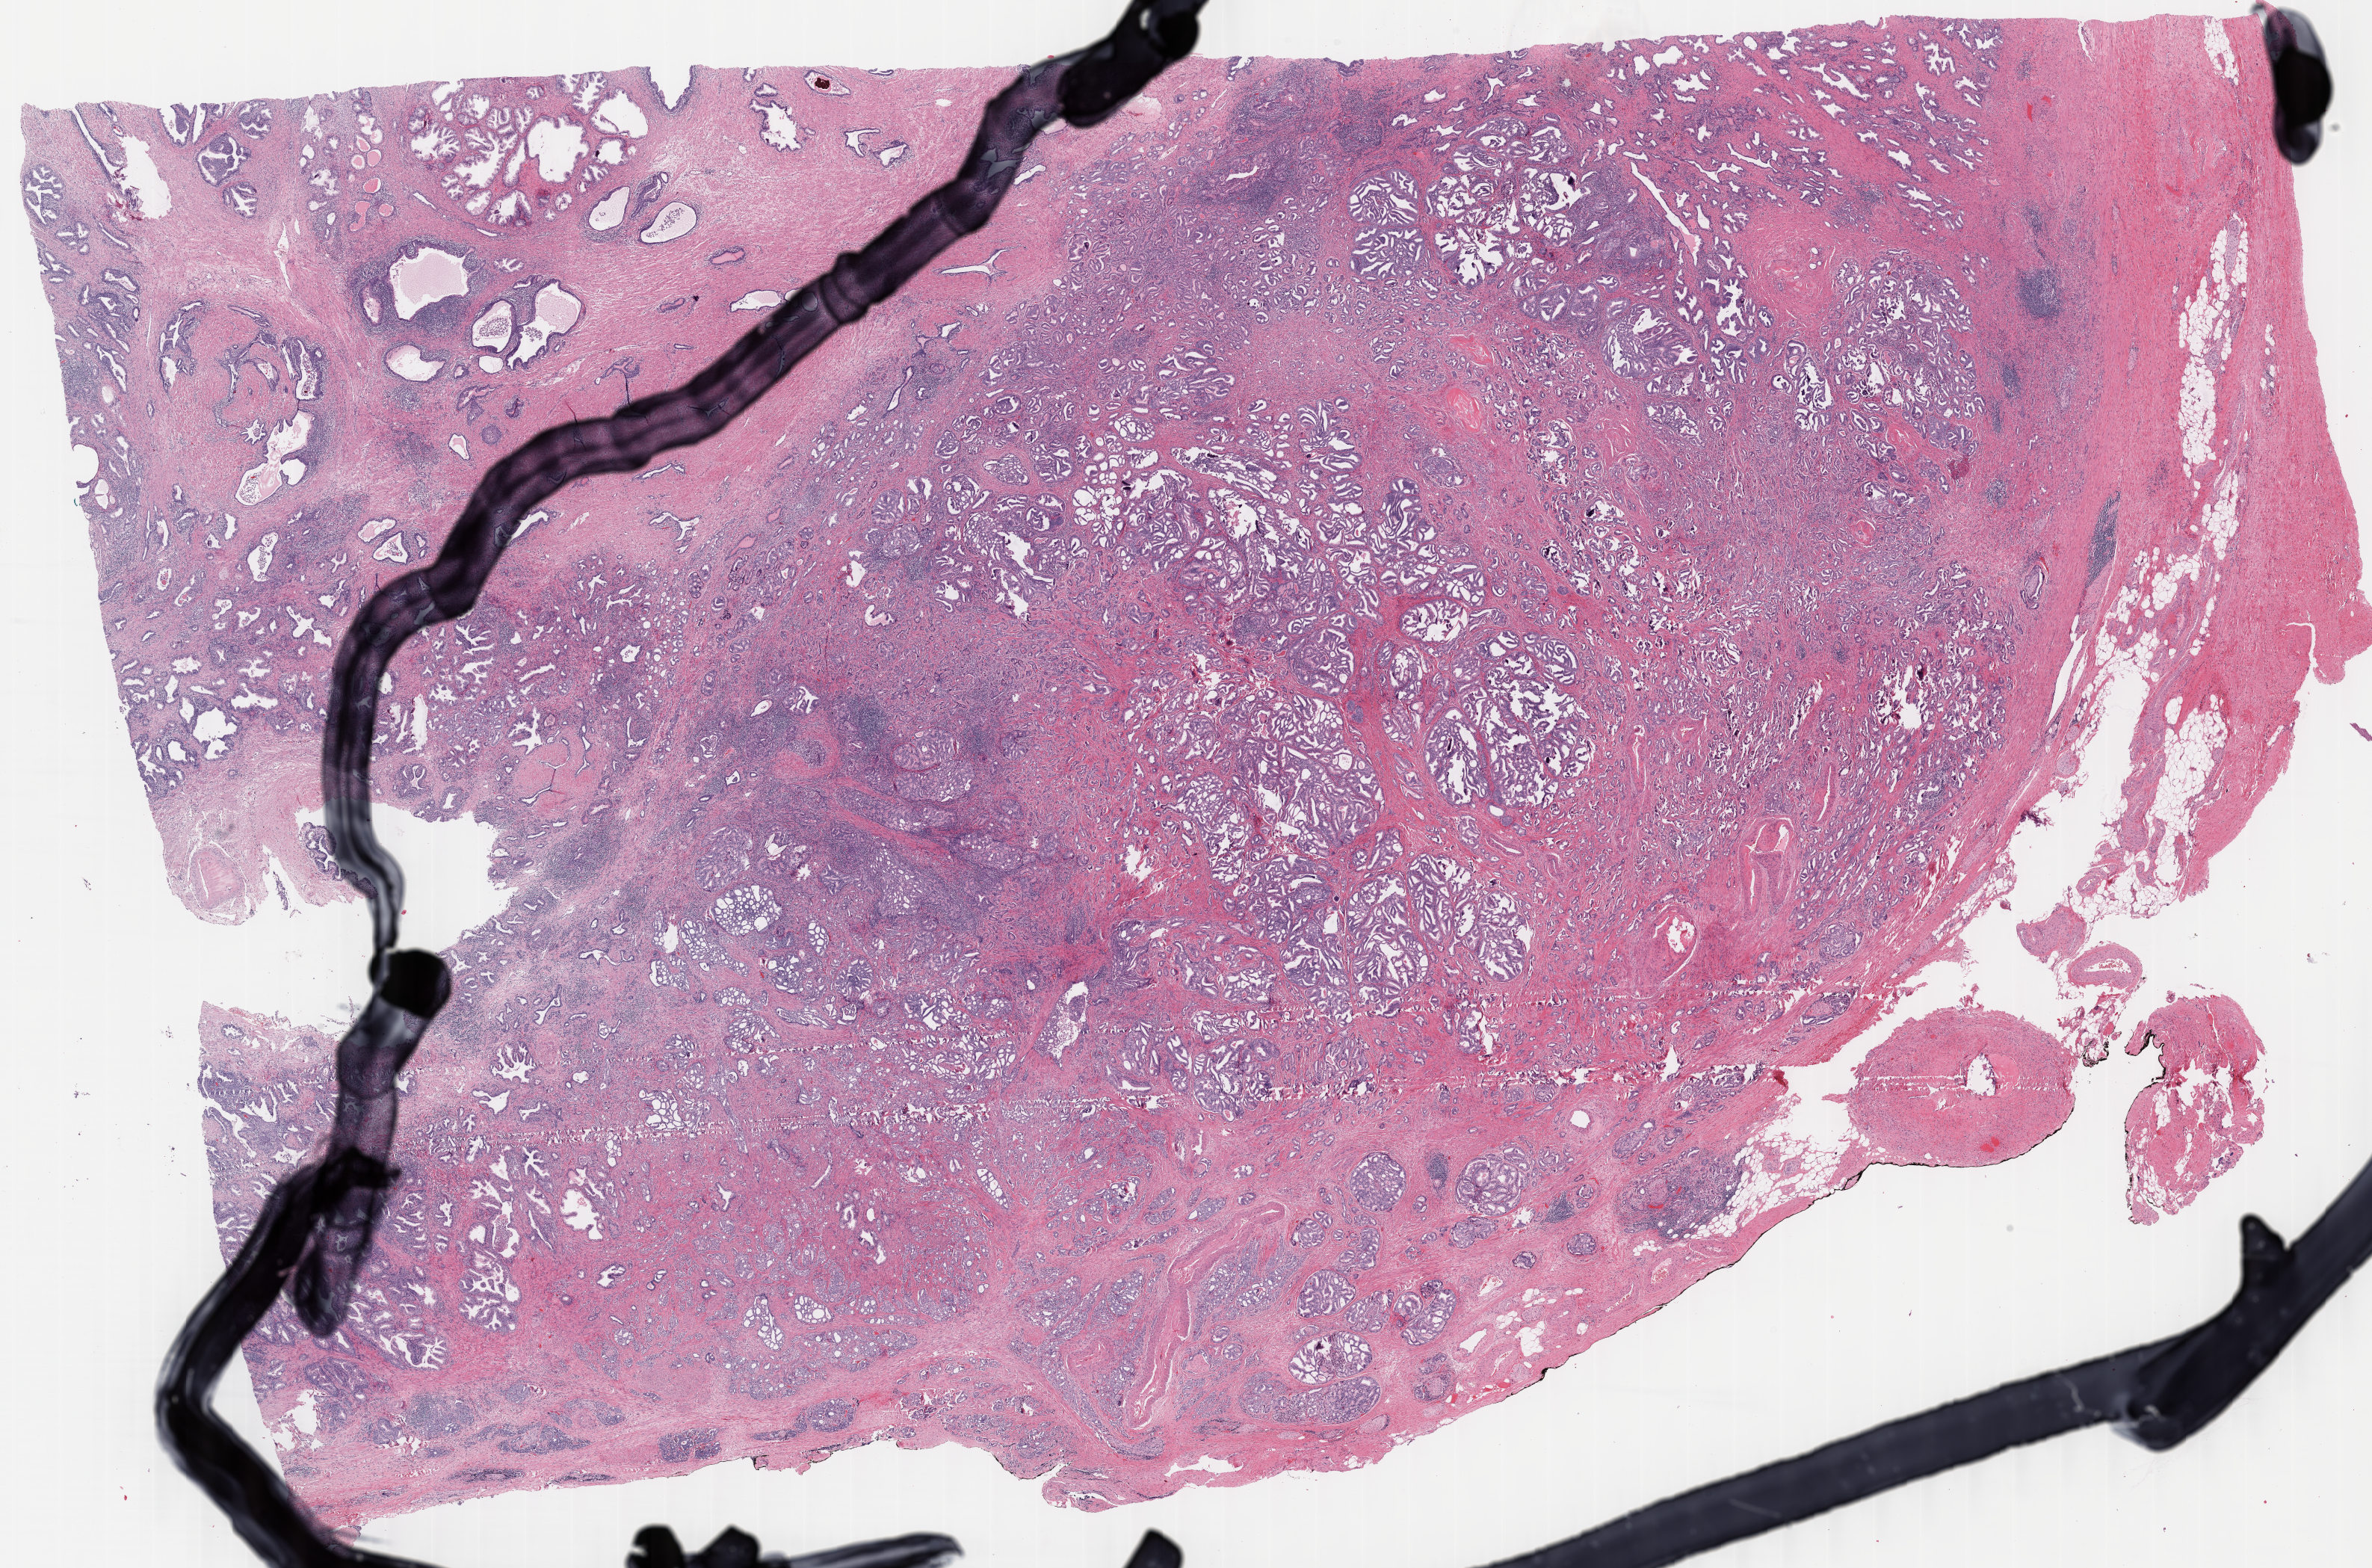
H&E whole-slide image, a low-resolution overview of the entire scanned area, about 25.2 x 16.7 mm; FFPE section; sample: primary tumour, prostate. Male, age 69 years at initial diagnosis. Gleason score: 8 (4+4).
Diagnosis: Adenocarcinoma, NOS (prostate gland).